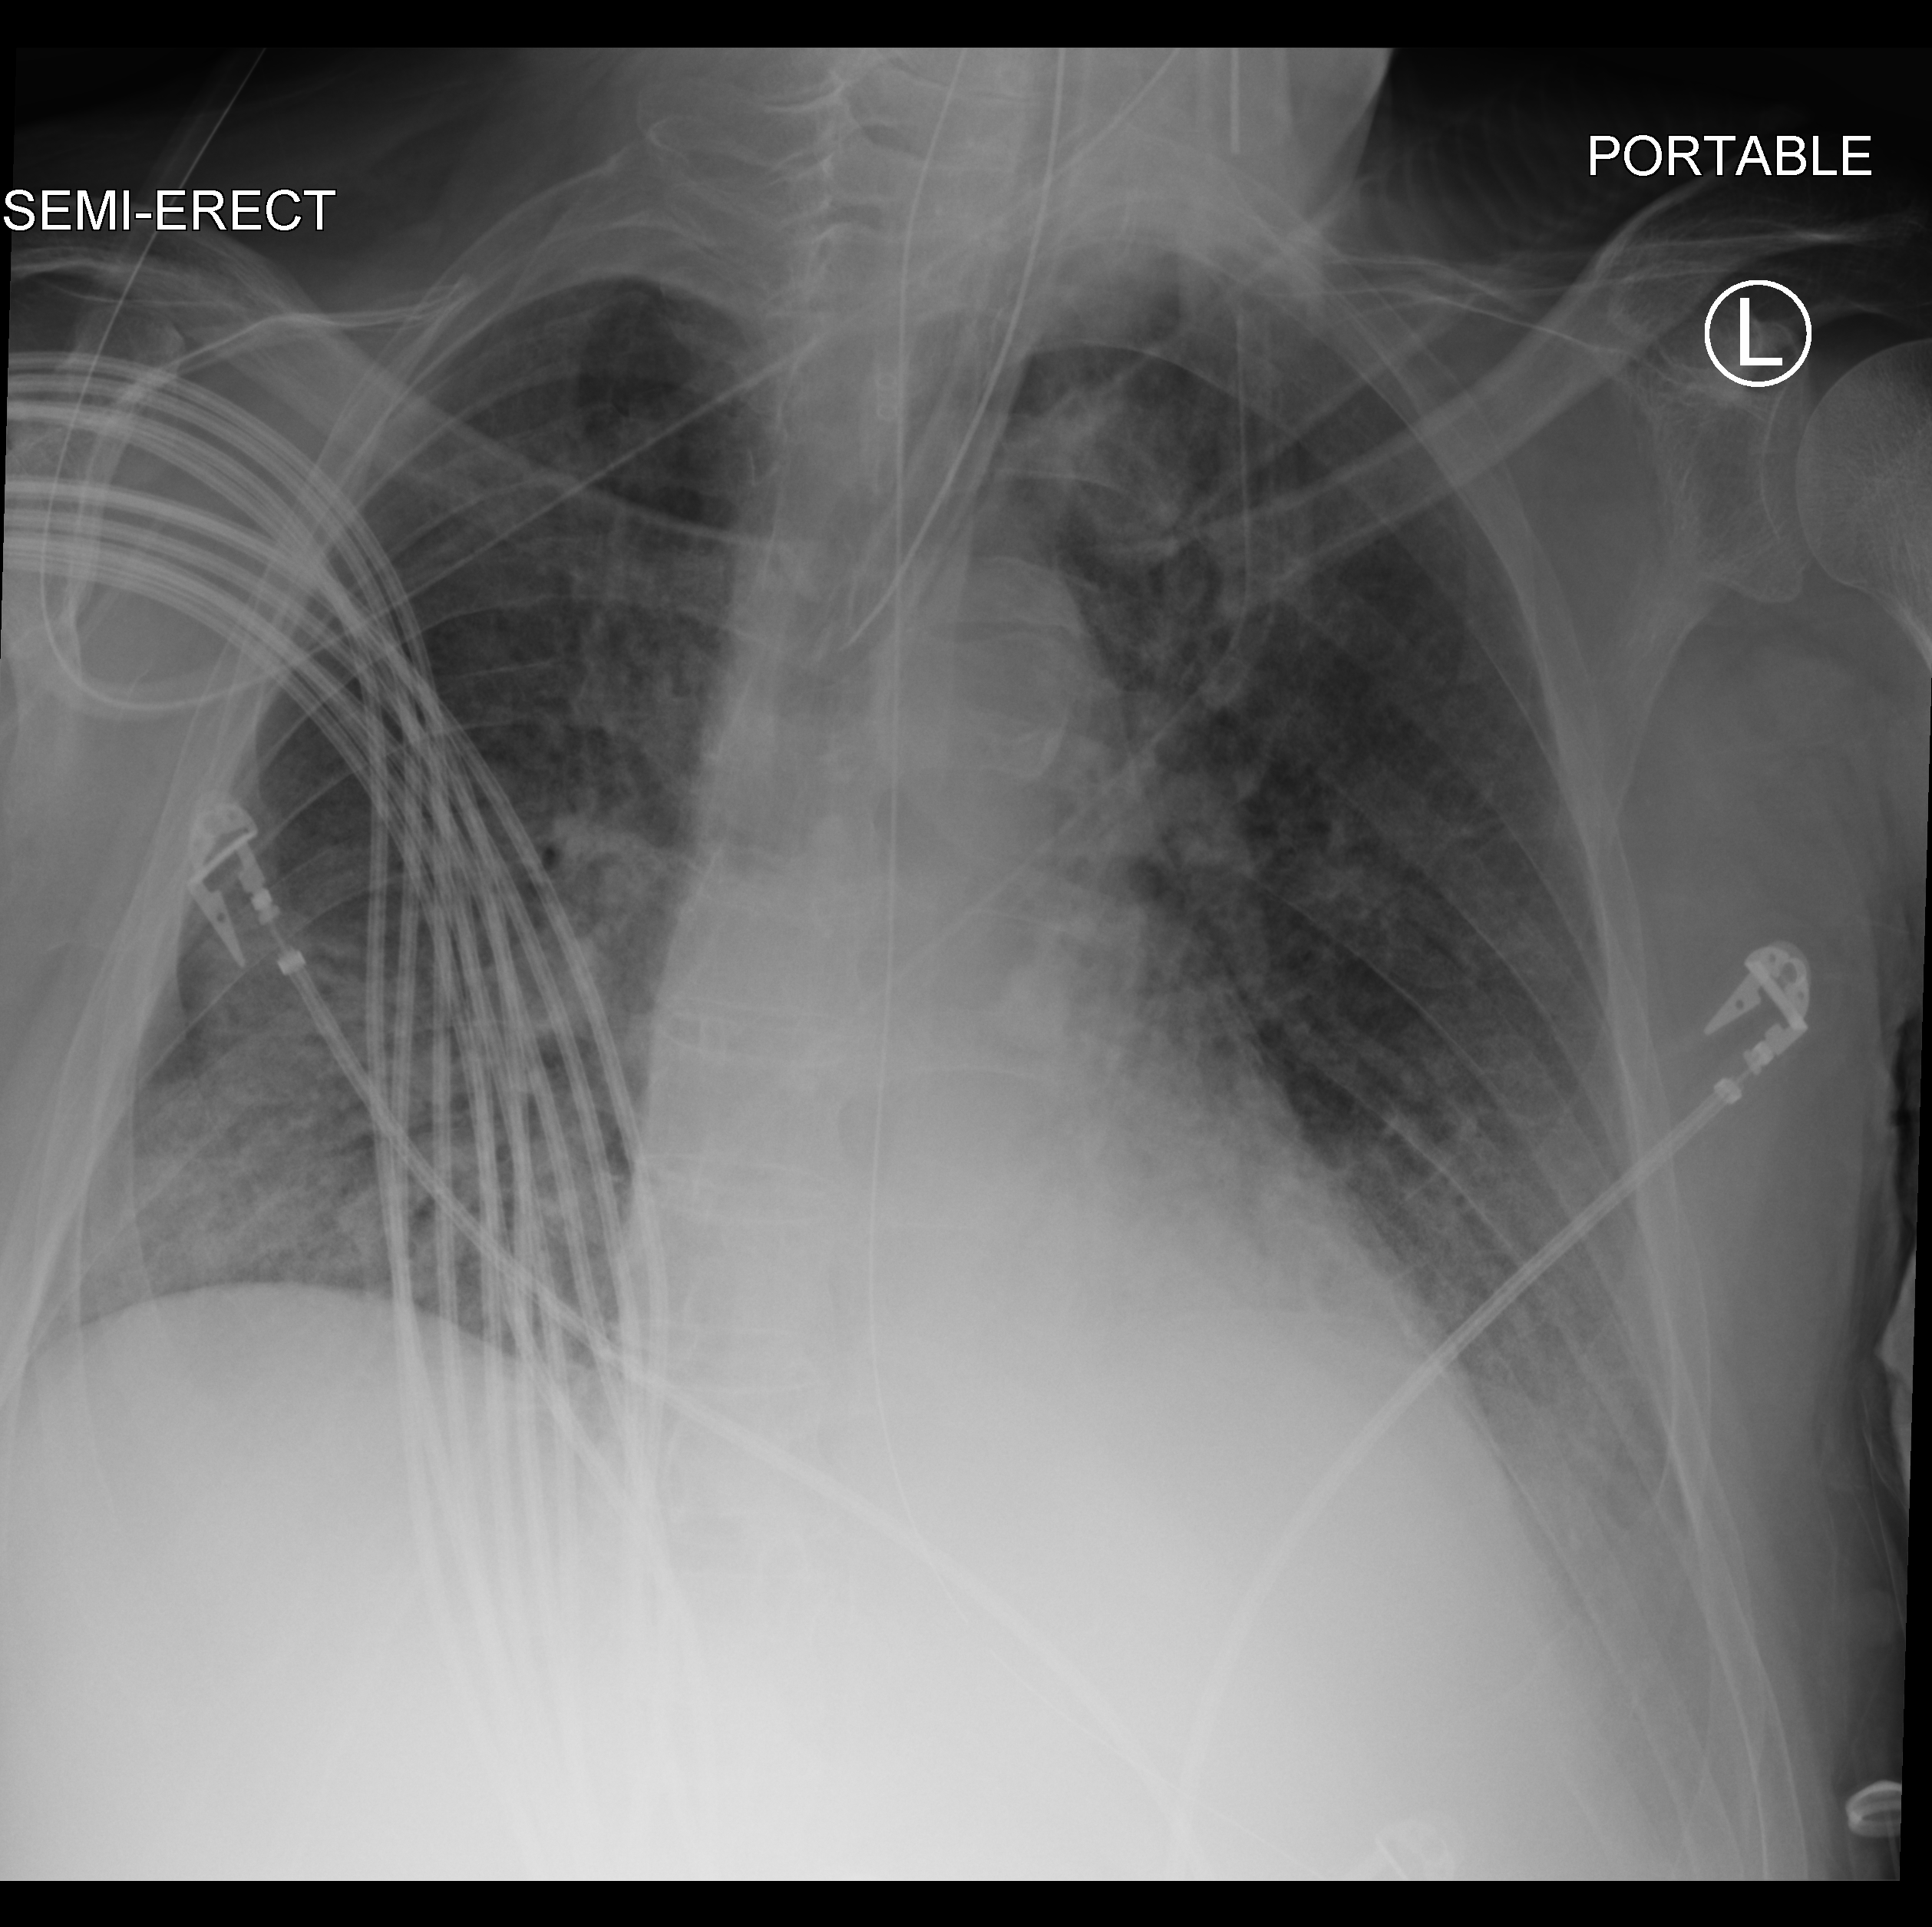
Chest X-ray (portable). Male patient hospitalised with COVID-19, age 60–74 years.
Hospital-stay facts (about this admission, not read from this image; timing relative to this image not recorded):
- mechanically ventilated during this hospital stay: yes